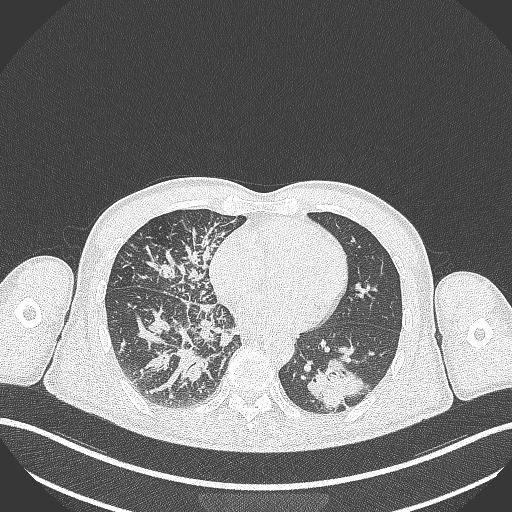
Chest CT, one axial slice; lung window (W 1500 / L -600 HU); 512 × 512 image matrix, field of view 400 × 400 mm. Male patient, age 49 years. Case-level facts recorded for this patient, not image findings: clinical TNM (as recorded): T2b N1 M0.
Structures marked on this image (rectangle marked by the reading radiologist):
- lung tumour (recorded histology: adenocarcinoma): bounding box <301,357,370,414> (left, top, right, bottom; pixels)